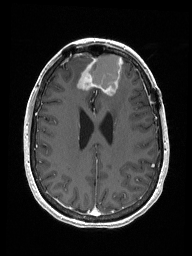
Brain MRI from a brain-tumour surgery series, one axial slice. Position 63 of 192 along the scan axis. T1-weighted post-contrast. 192 × 256 image matrix, field of view 187 × 250 mm. From the clinical record (not read from this slice): histopathology: Metastastic Carcinoma from Breast primary; tumour location: Right Frontal.
Annotated regions visible in this slice (outlined manually by an expert reader):
- previous resection cavity: bounding box <89,54,123,94> (left, top, right, bottom; pixels)